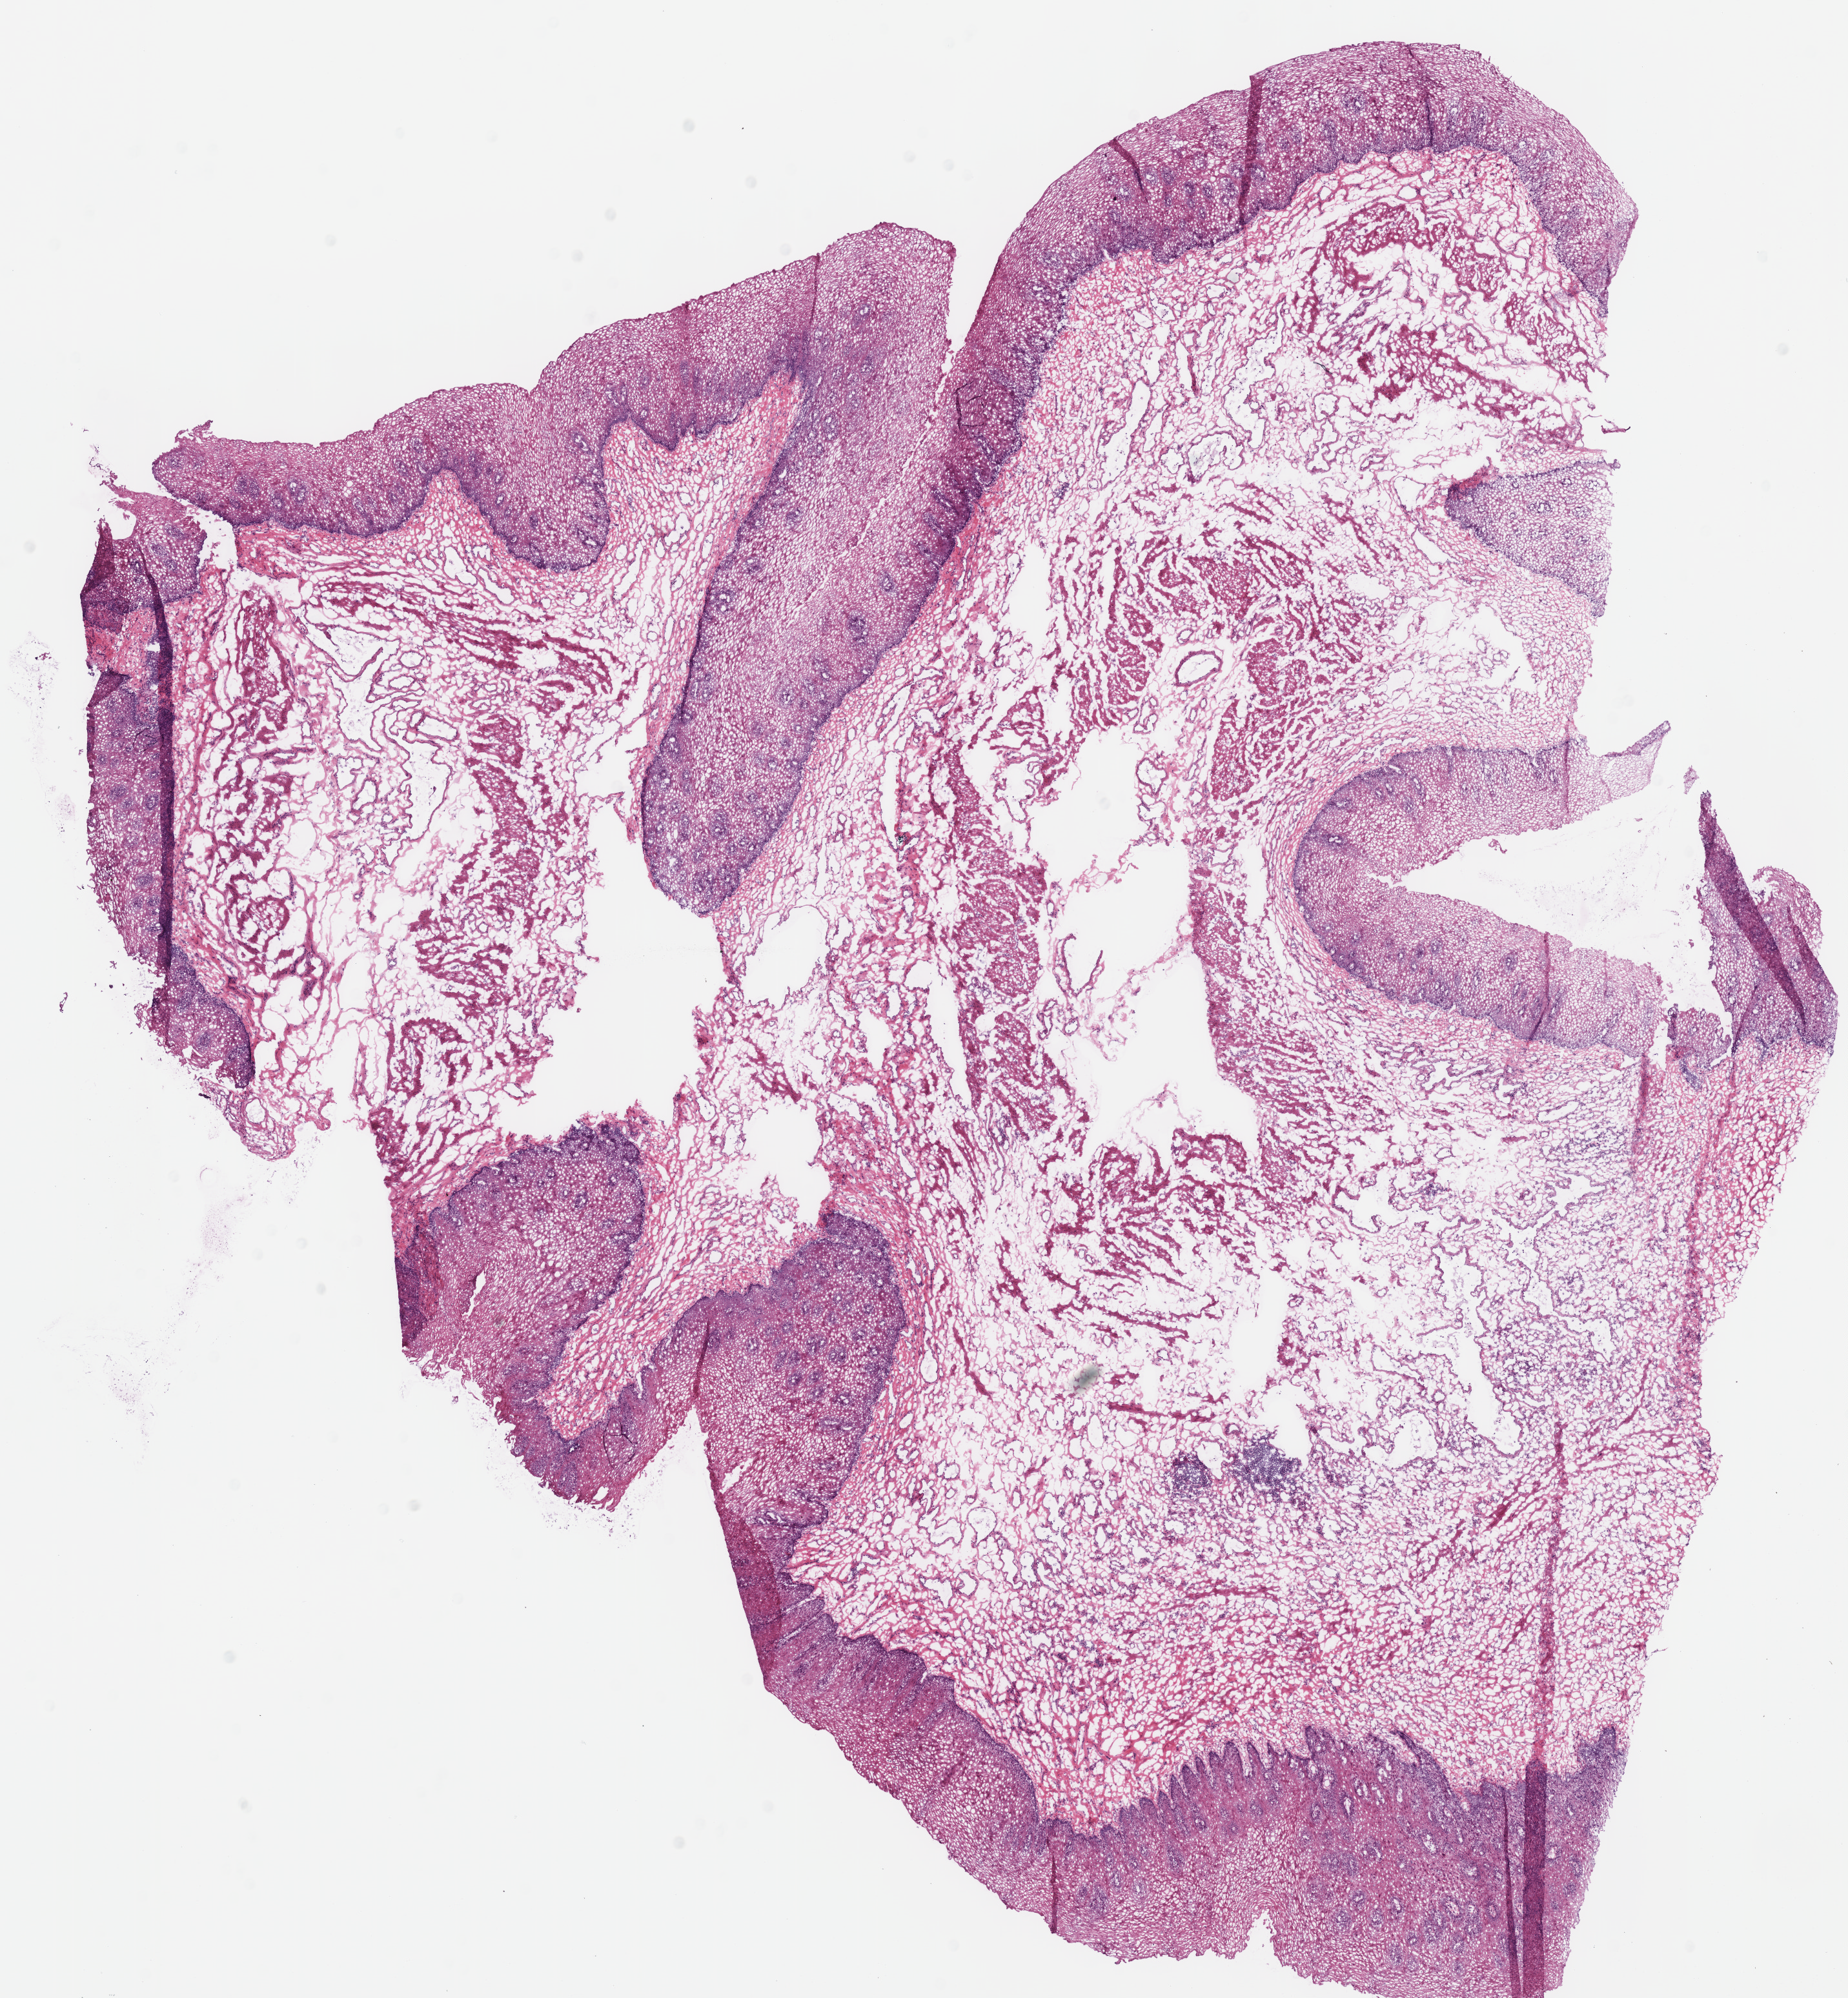
Whole-slide histology image, Hematoxylin and eosin (H&E) stained, a low-resolution overview of the entire scanned area, about 11.3 x 12.2 mm. Frozen section from the top of the tissue portion. Stomach, solid tissue normal (non-tumour tissue) sample. Male, age 68 years at initial diagnosis.
This section: solid tissue normal sample (biorepository sample class). Patient diagnosis: Adenocarcinoma, NOS.